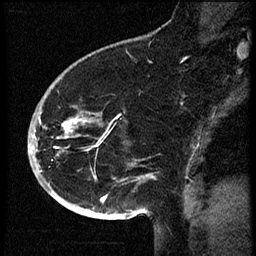
Breast MRI (dynamic contrast-enhanced), one sagittal slice. Position 40 of 60 along the scan axis. Dynamic contrast-enhanced study with each time point stored as its own series, time point 2 of 3 at this slice position (early post-contrast, ordered by acquisition time). 1.5 T. TE 4.2 ms, TR 18.9 ms. 2 mm slice thickness. 256 × 256 image matrix. Female patient. Case-level facts recorded for this patient, not image findings: setting: breast cancer imaged before/during neoadjuvant chemotherapy; receptor status: HR-positive, HER2-negative.
Annotated regions visible in this slice (semi-automatic segmentation, software-assisted and operator-edited):
- analysis volume of interest (the breast-tissue region the enhancement analysis was run in; not a lesion): box from (x=31, y=87) to (x=105, y=173) px
- tumour enhancement mask (voxels above the 100 % enhancement threshold inside the analysis volume of interest): (x=31, y=119)–(x=84, y=150)